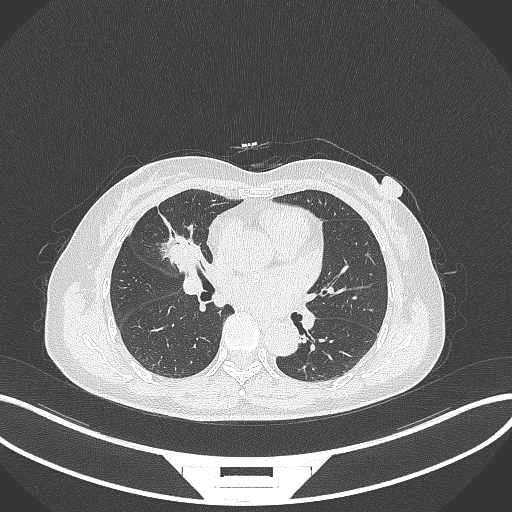
Chest CT, one axial slice. Slice 154 of 284 in the series (ordered by position). Reconstruction kernel B70f. 120 kVp. Lung window (W 1500 / L -600 HU). 512 × 512 image matrix. Patient: female, 51 years. From the clinical record (not read from this slice): clinical TNM (as recorded): T1c N0 M0; histopathological grade: G2.
Outlined on this slice (bounding box drawn by a radiologist):
- lung tumour (recorded histology: adenocarcinoma): bounding box (x1, y1, x2, y2) in pixels: (158, 228, 201, 278)